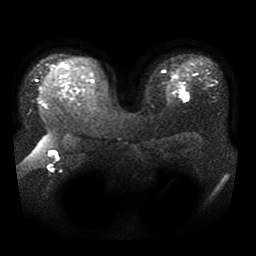
Breast MRI, one axial slice; slice 29 of 41 in the series (ordered by position); diffusion-weighted series; image 2 of 4 stored at this slice position (different b-values; order by instance number); 1.5 T; 5 mm slice thickness; 256 × 256 image matrix. Female patient.
Annotated regions visible in this slice (outlined manually by an expert reader):
- tumour on diffusion-weighted imaging: box from (x=186, y=94) to (x=189, y=100) px